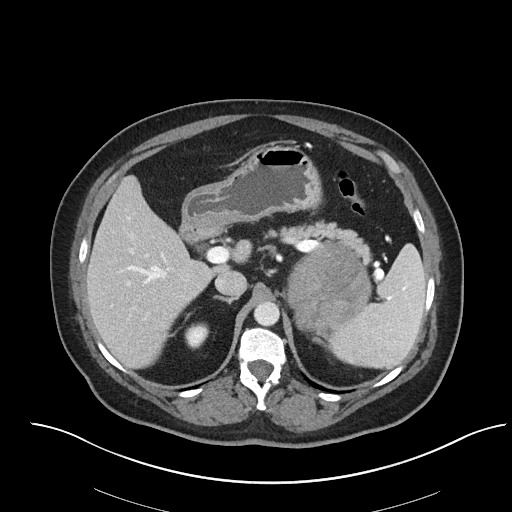
Contrast-enhanced abdominal CT, one axial slice; slice 54 of 92 in the series (ordered by position); 120 kVp; intravenous contrast given; soft-tissue window (W 400 / L 40 HU); 3 mm slice thickness; 512 × 512 image matrix. Patient: female, 53 years. Case-level facts recorded for this patient, not image findings: diagnosis: adrenocortical carcinoma; tumour side: left adrenal; tumour size at pathology: 9 cm.
Structures marked on this image (semi-automatic segmentation, software-assisted and operator-edited):
- mass: bounding box [x1, y1, x2, y2] px = [288, 246, 370, 336]